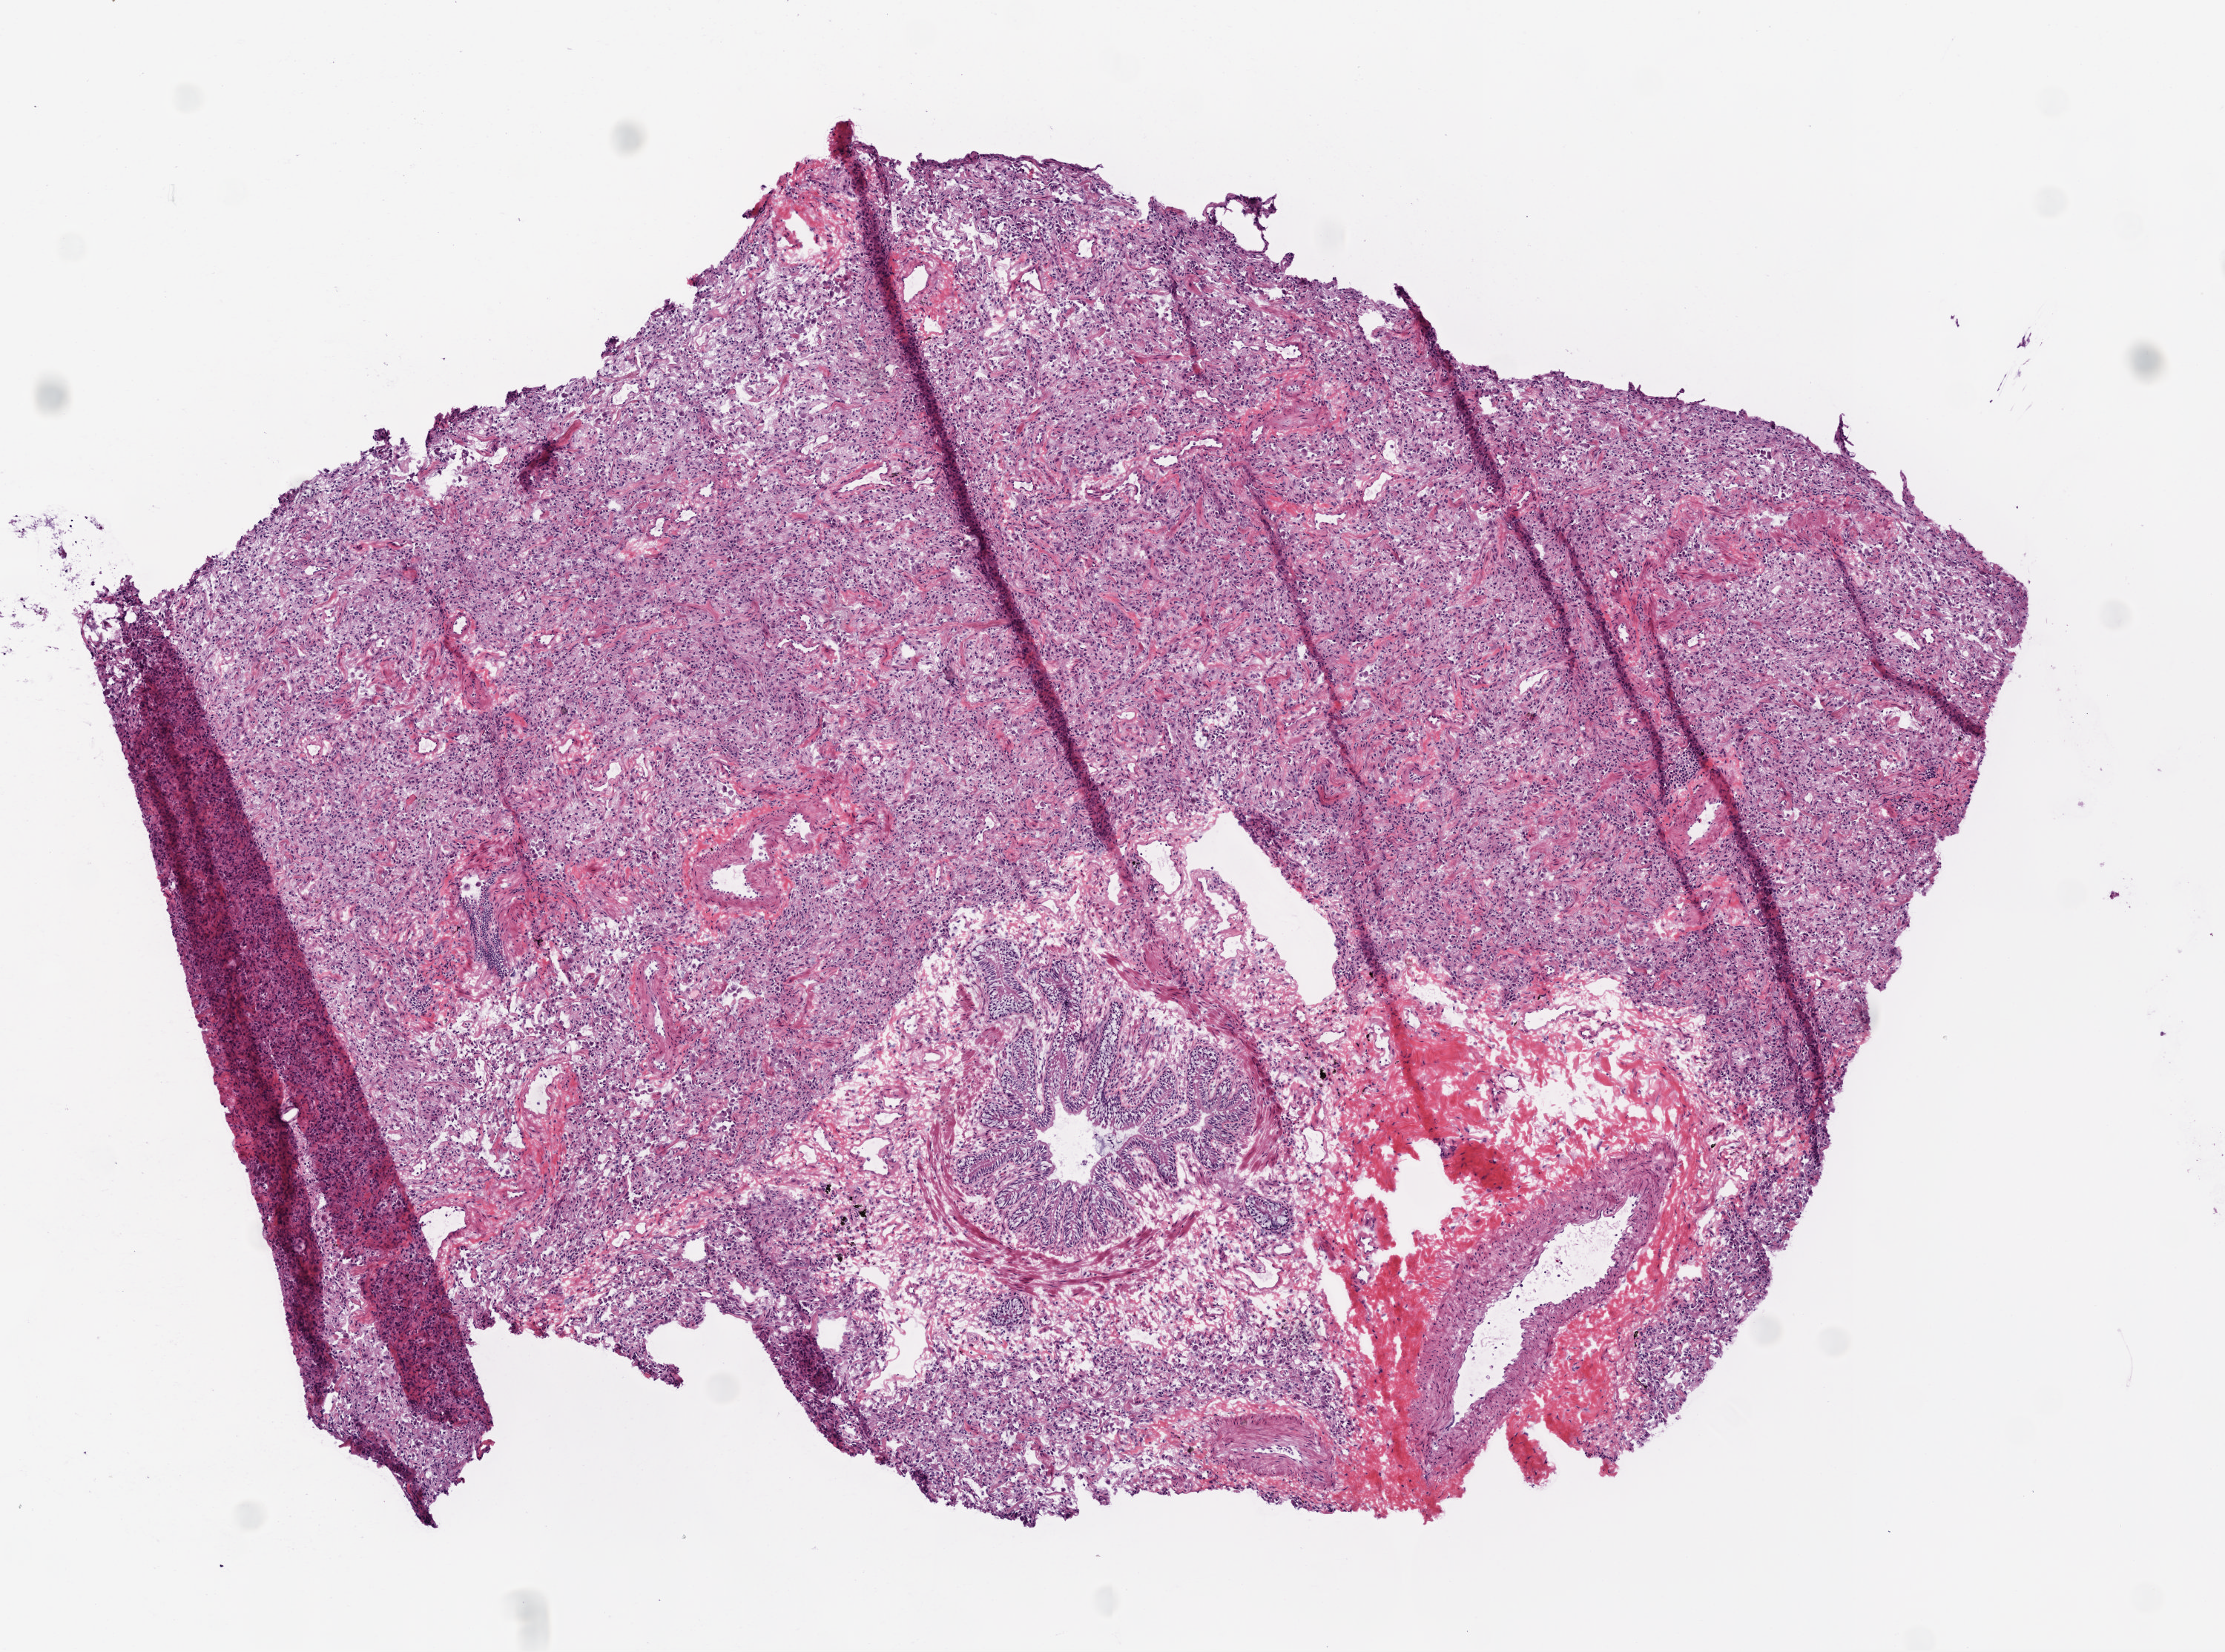
H&E-stained whole-slide image, shown as a low-resolution overview of the whole scanned area (about 6.0 x 4.5 mm, slide scanned at 20x). Frozen section. Lung, solid tissue normal (non-tumour tissue) sample. Male, age 66 years at initial diagnosis.
• this section: solid tissue normal (non-tumour) sample from the same patient
• patient diagnosis: Squamous cell carcinoma, NOS